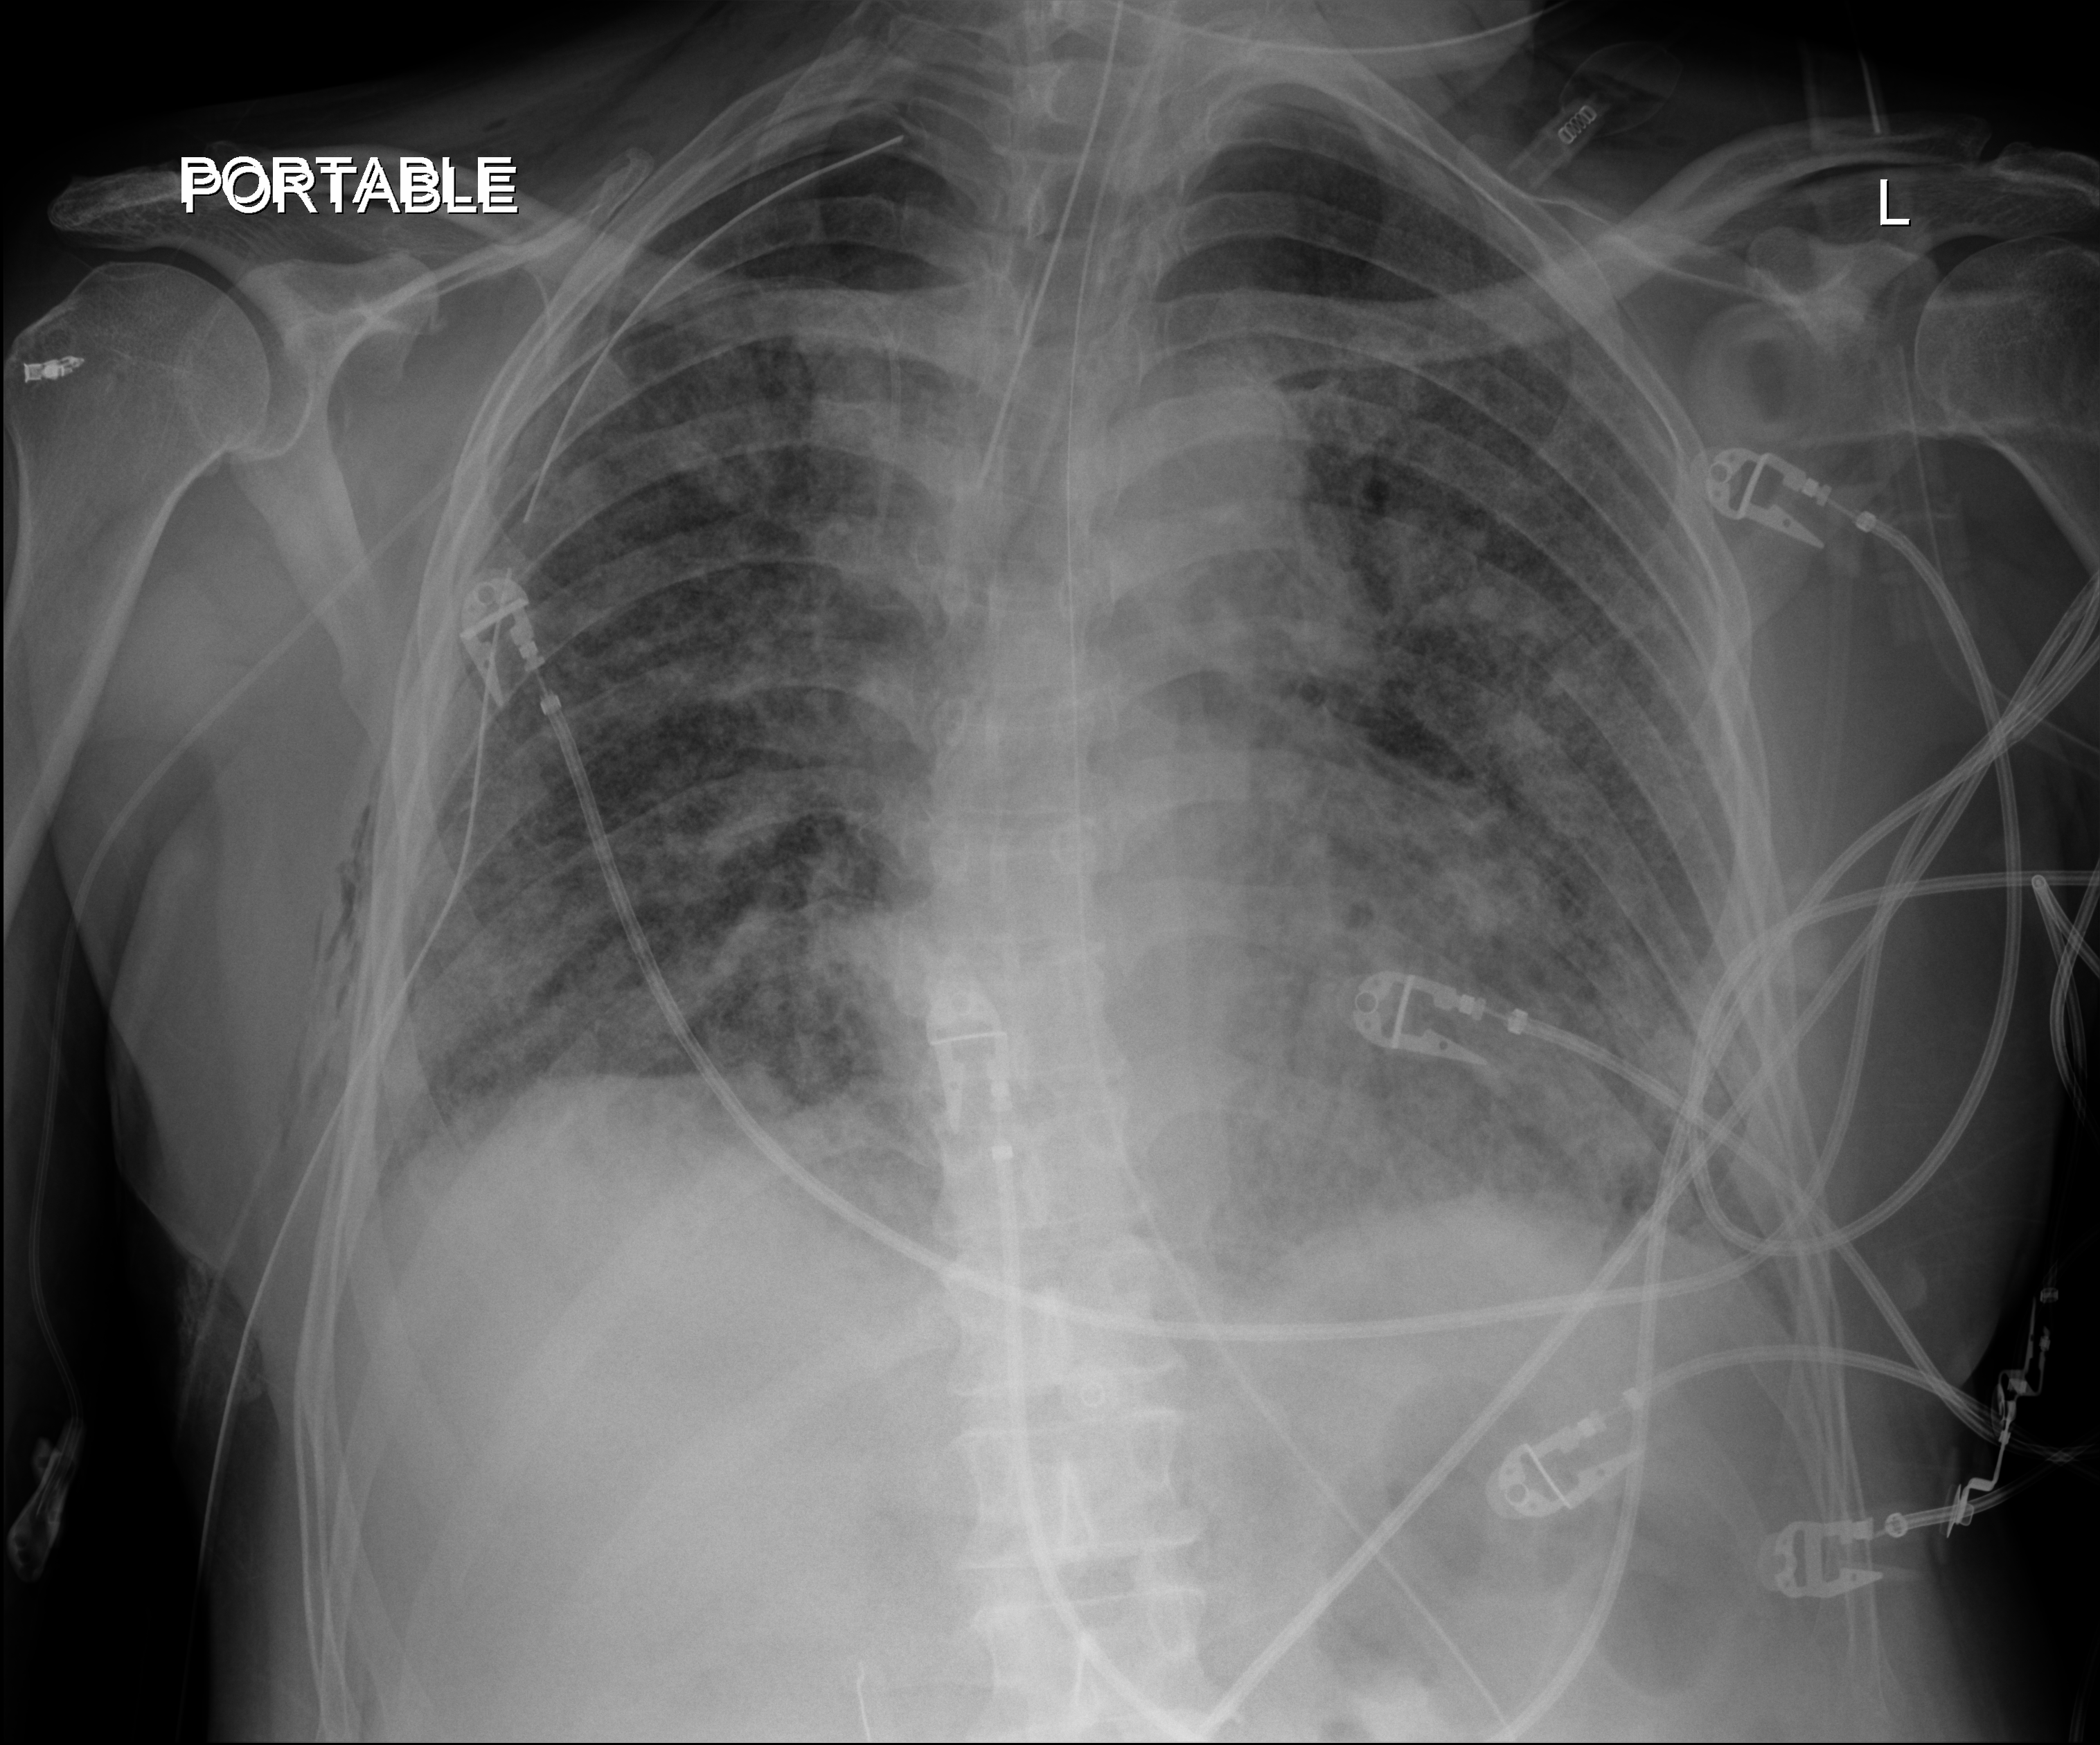
Portable chest radiograph; anteroposterior (AP) projection. Male patient hospitalised with COVID-19, age 60–74 years.
Admission-level facts for this patient (not findings on this image; timing relative to this image not recorded): admitted to intensive care during this hospital stay: yes; mechanically ventilated during this hospital stay: yes.